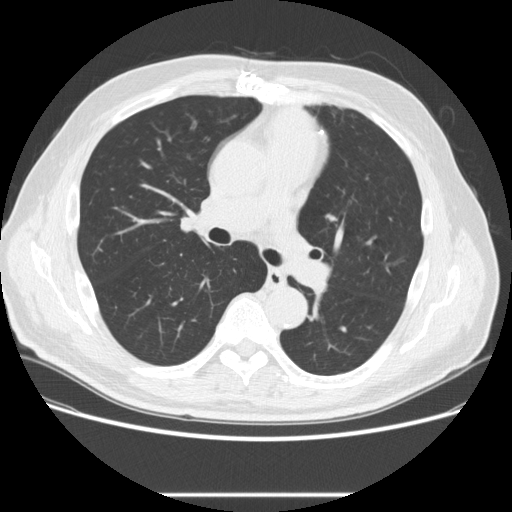
Low-dose screening chest CT, axial slice. Second annual screen. Lung window (W 1500 / L -600 HU). 2.5 mm slice thickness. Male, age 66 years at enrolment.
• Expert-annotated lung lesion, bounding box <320,202,350,233> (left, top, right, bottom; pixels).
• Screening reader's record for this exam (one nodule recorded; not confirmed to be the boxed lesion): non-calcified nodule or mass ≥4 mm, right lower lobe, 4 × 4 mm, smooth margins, soft tissue attenuation, pre-existing on the prior screen: yes; interval growth: no.
• Note: the box lies in the patient's left hemithorax on this image, whereas the reader's record names the right lung; they may be different findings.
• Official screen result: positive, no significant change: stable abnormalities potentially related to lung cancer, unchanged since the prior screening exam.
• Participant outcome: lung cancer diagnosed 449 days after this screen — squamous cell carcinoma, NOS, left upper lobe, poorly differentiated (G3), stage IA (AJCC 6th edition), 27 mm at pathology.